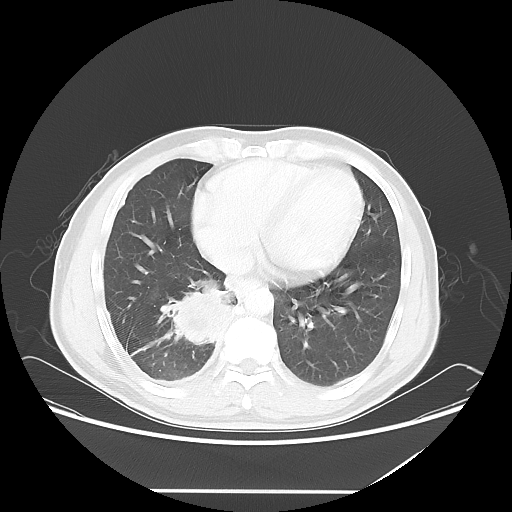
Chest CT, one axial slice. Slice 22 of 60 in the series (ordered by position). Lung window (W 1500 / L -600 HU). 5 mm slice thickness. 512 × 512 image matrix, field of view 419 × 419 mm. Male patient, age 48 years. From the clinical record (not read from this slice): clinical TNM (as recorded): T3 N3 M1a.
Annotated regions visible in this slice (bounding box drawn by a radiologist):
- lung tumour (recorded histology: squamous cell carcinoma): bounding box <158,273,237,350> (left, top, right, bottom; pixels)